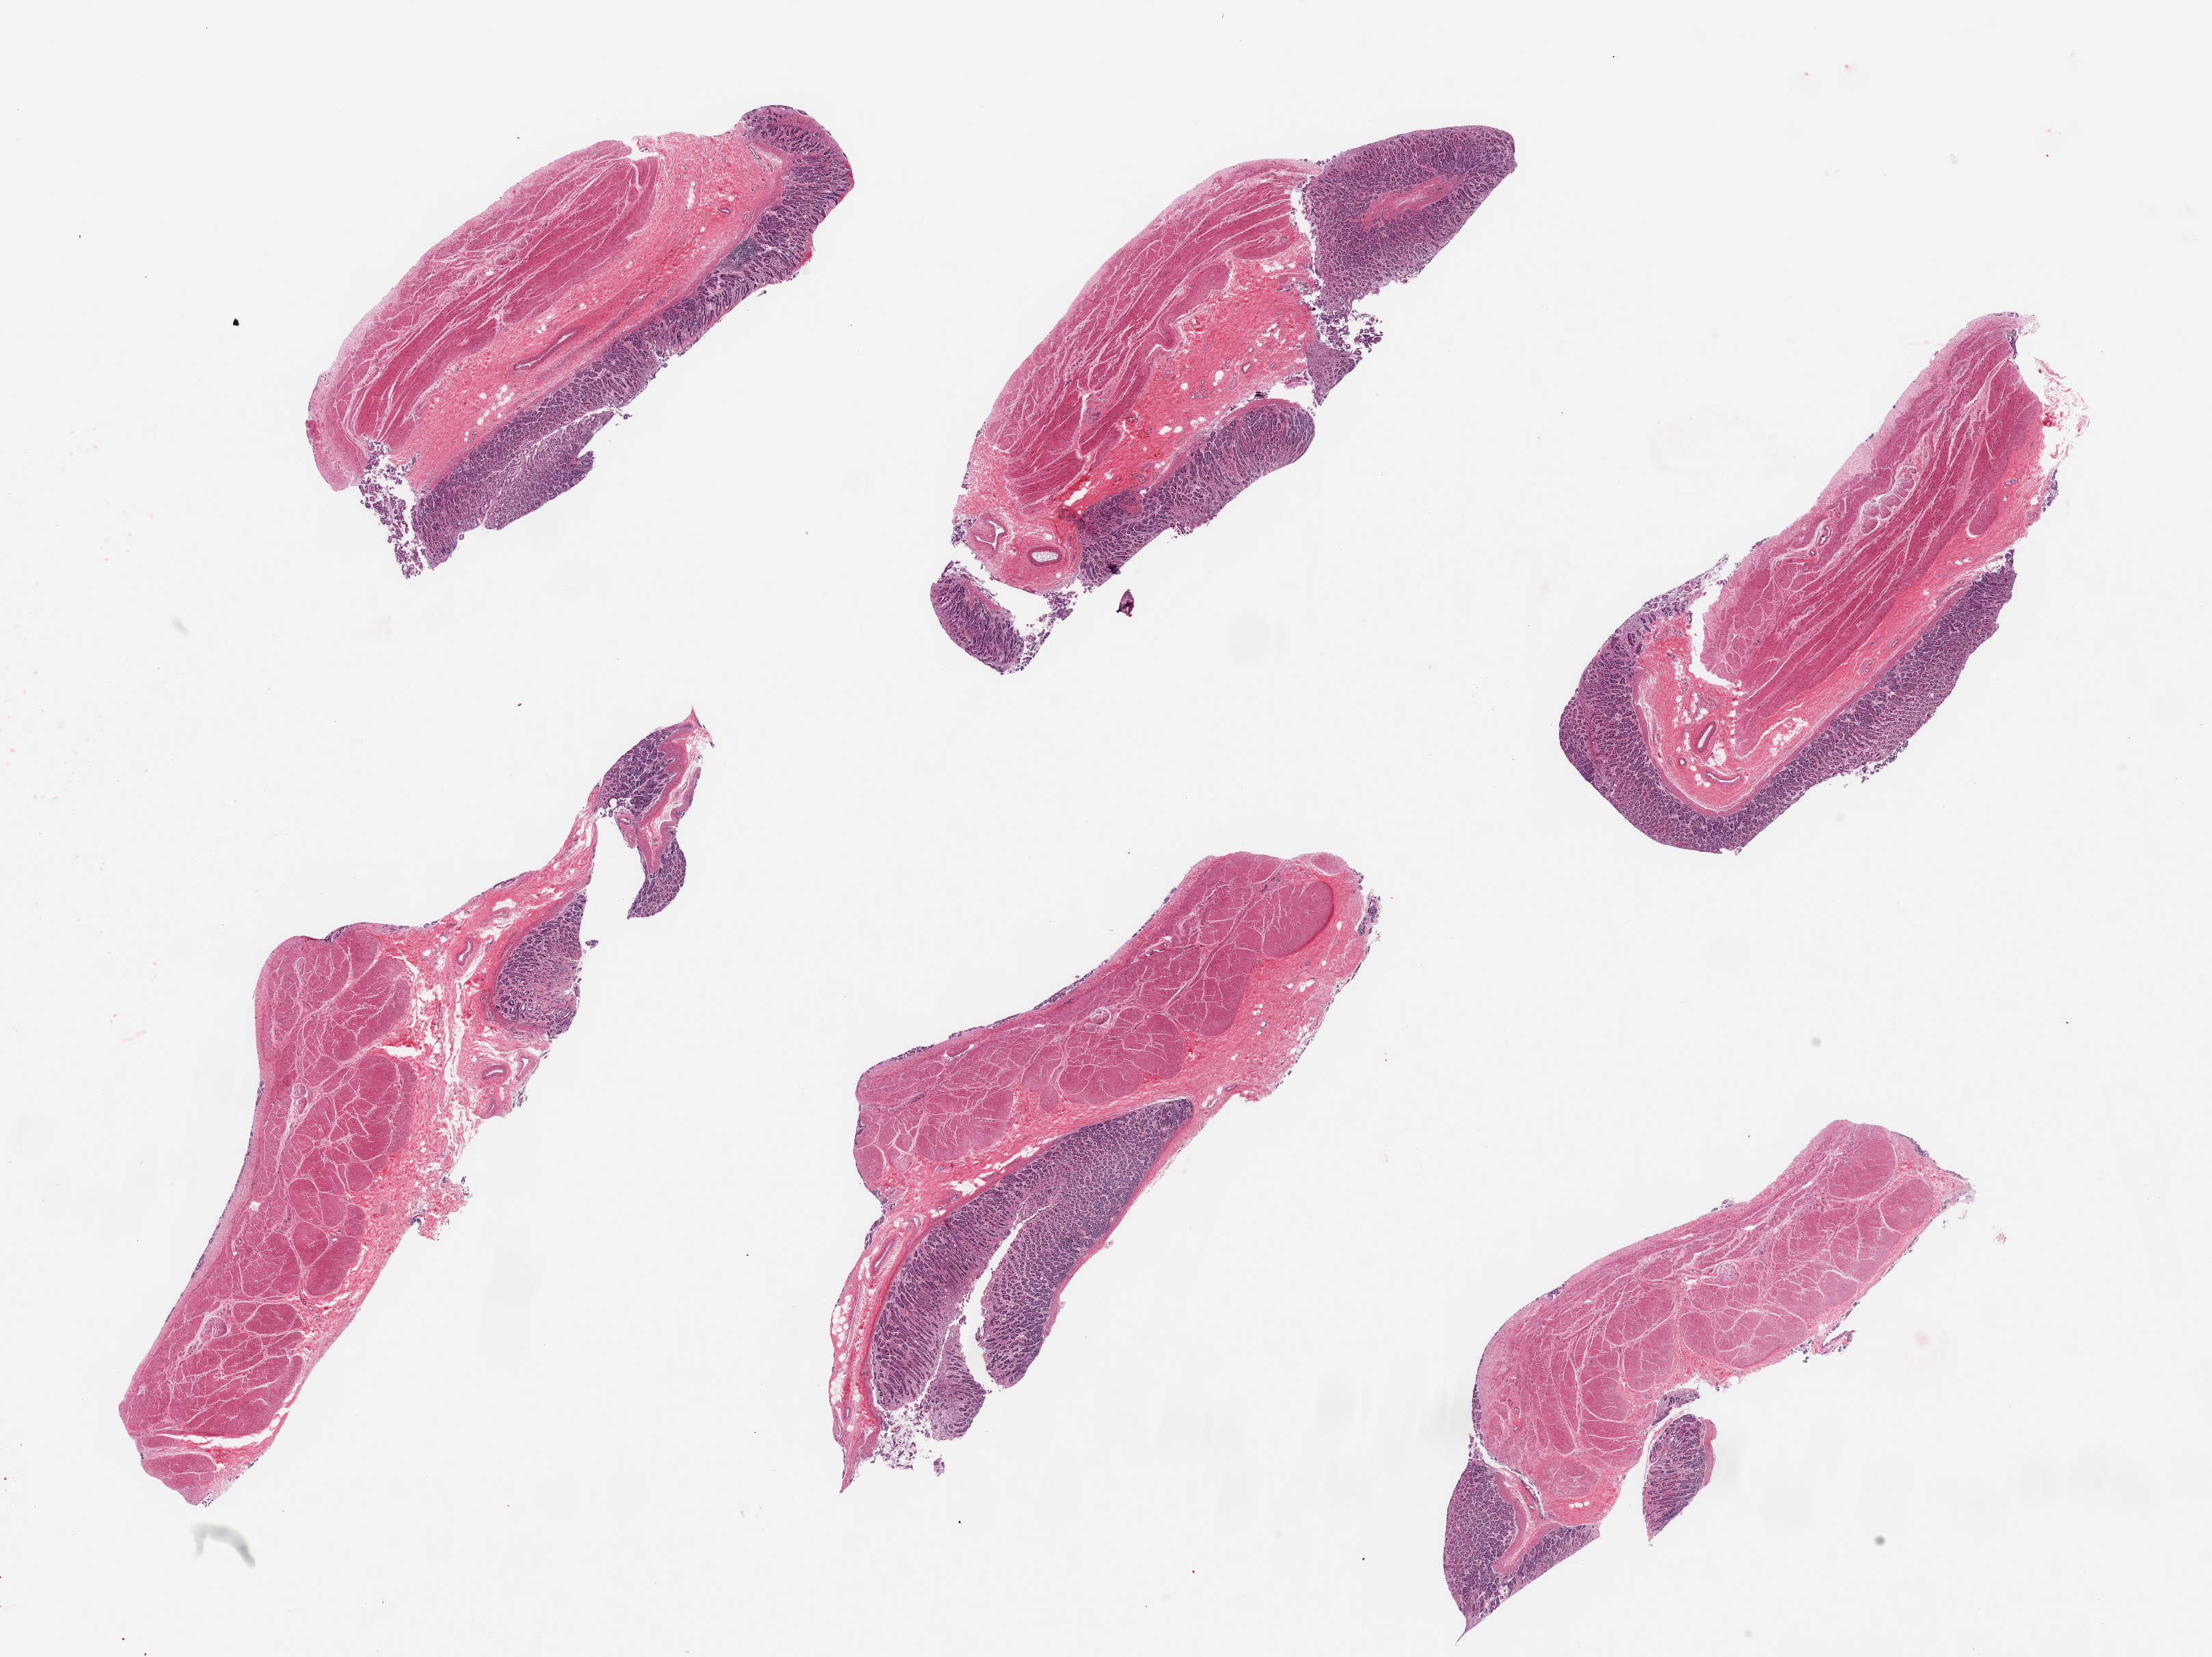
Whole-slide image, hematoxylin and eosin (H&E) stain, whole scanned area (about 25.6 x 19.2 mm) shown as a low-resolution overview, PAXgene-fixed, paraffin-embedded tissue, target tissue: stomach, donor tissue sample. Donor sex: female.
Review note (as recorded): 6 pieces; mild to moderate autolysis of gastric mucosa; well preserved muscularis.